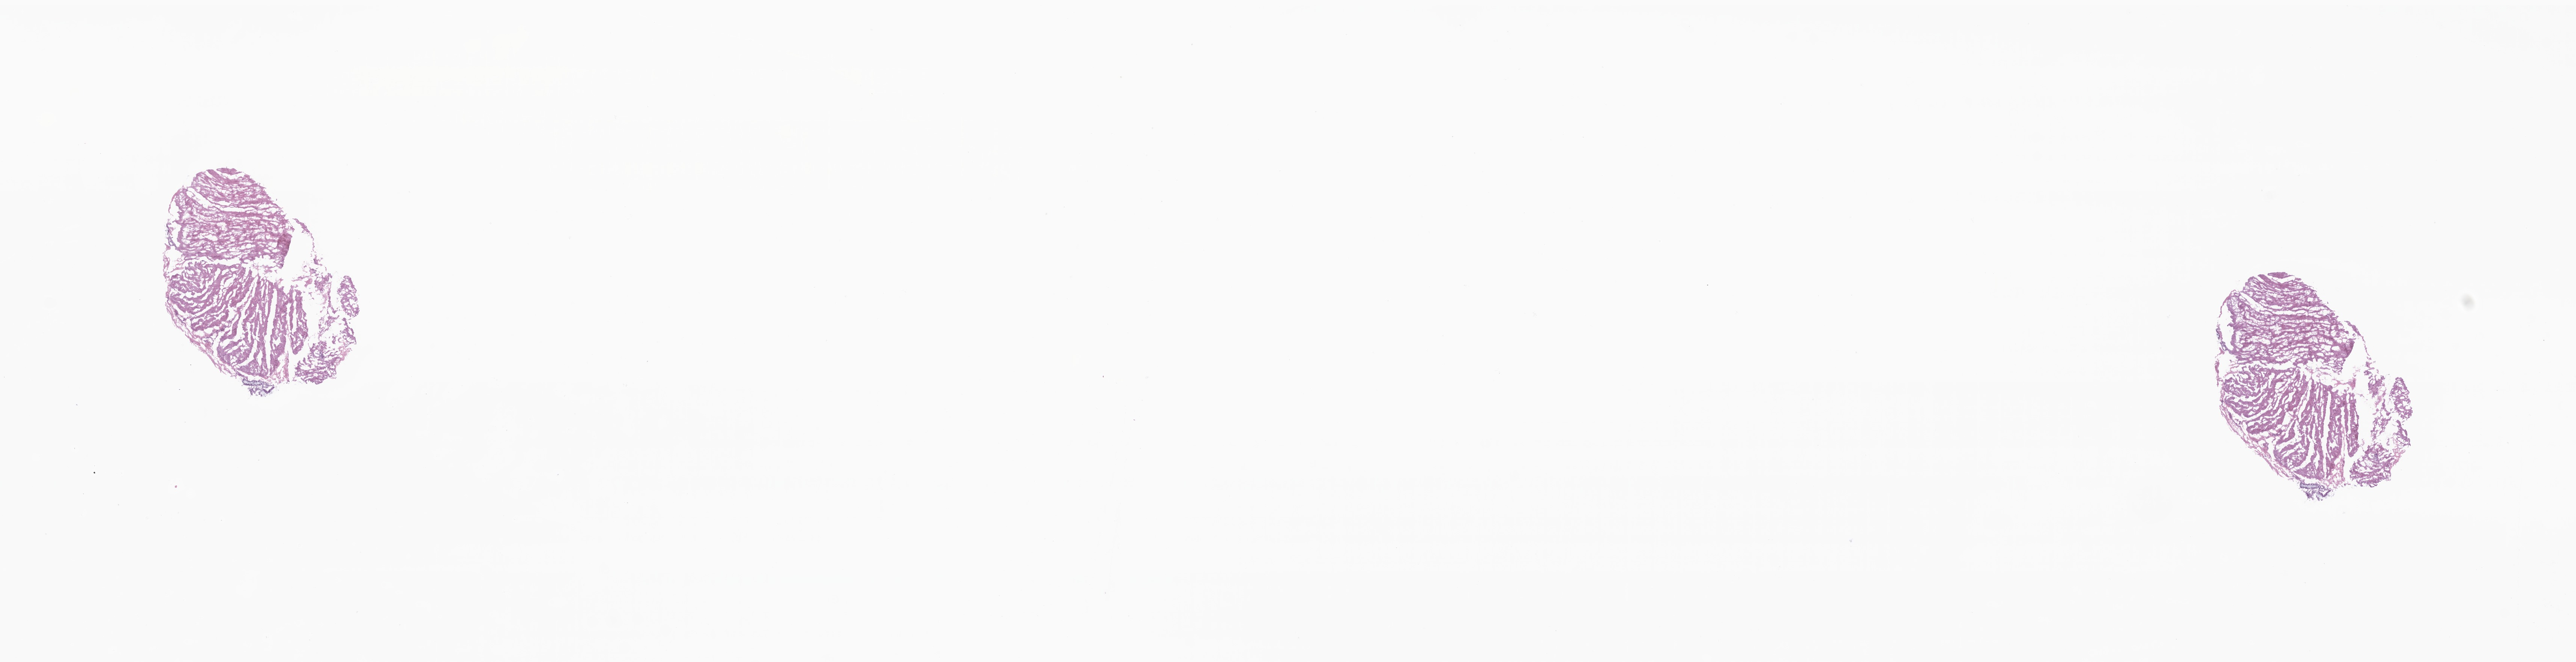
Digitized hematoxylin and eosin (H&E)-stained section — a low-resolution overview of the entire scanned area, about 28.9 x 7.4 mm; frozen section; specimen: non-tumor (normal tissue) sample from a patient with adenocarcinoma, NOS; anatomic site: rectosigmoid junction. Patient sex: female. Composition of this section per pathologist review: tumor cells 0%, tumor nuclei 0%, stromal cells 100%, necrosis 0%, normal cells 0%. Infiltration values recorded for this section: lymphocyte infiltration 0%, monocyte infiltration 0%, neutrophil infiltration 0%.
This section: non-tumor tissue sample; the patient's diagnosis is given above. Section: bottom of the tissue portion.